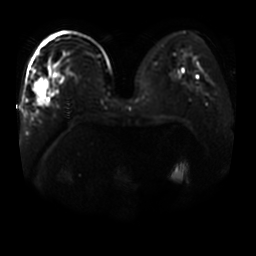
Breast MRI, one axial slice. Position 21 of 44 along the scan axis. Diffusion-weighted series; image 2 of 4 stored at this slice position (different b-values; order by instance number). 3 T. 256 × 256 image matrix, field of view 400 × 400 mm. Female patient.
Outlined on this slice (expert manual segmentation):
- tumour on diffusion-weighted imaging: bounding box <35,78,48,105> (left, top, right, bottom; pixels)